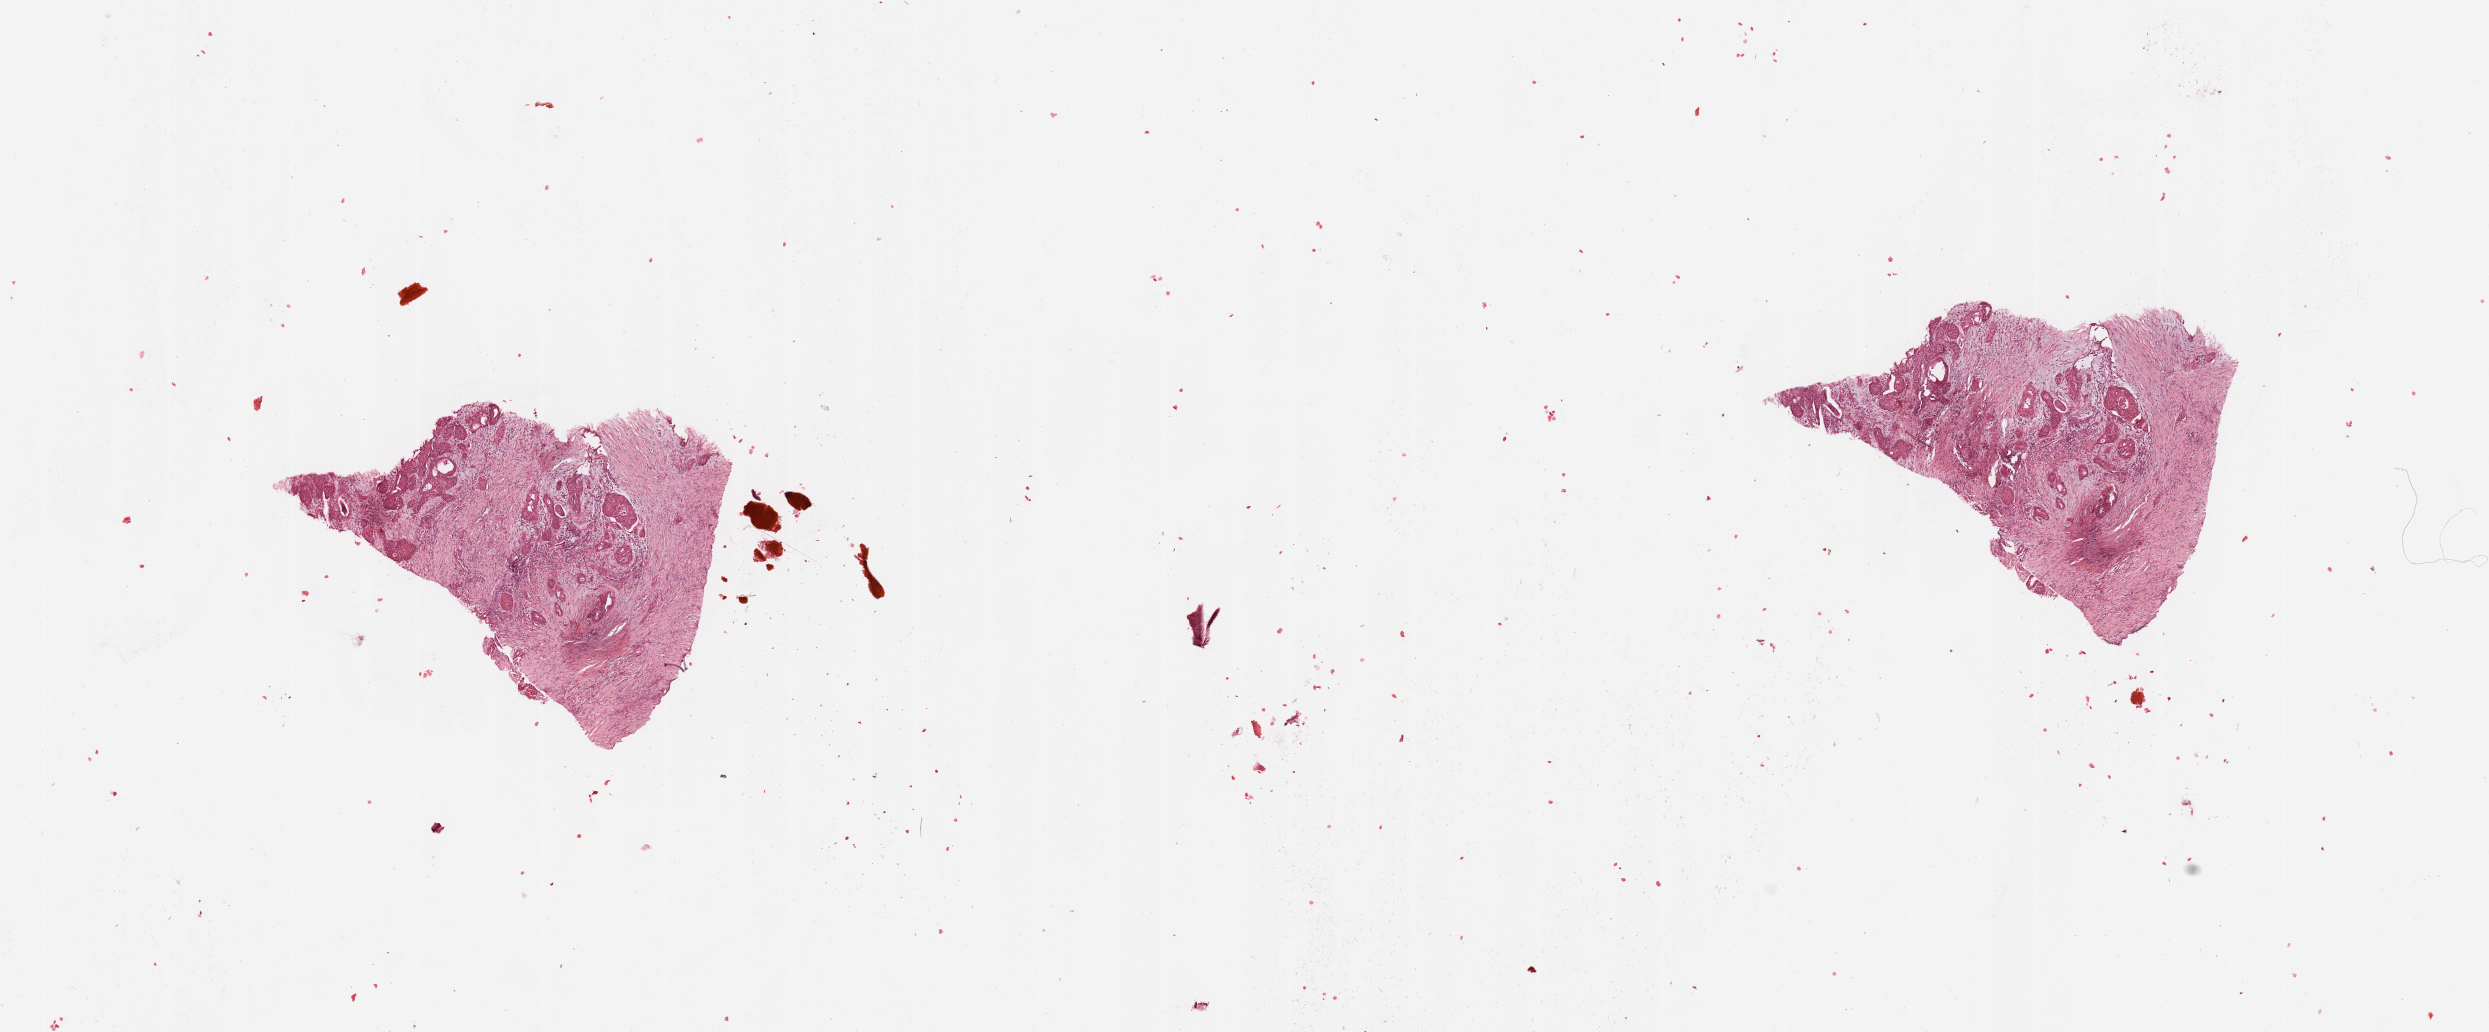
Digitized H&E tissue section (whole slide) — shown as a low-resolution overview of the whole scanned area (about 19.7 x 8.2 mm), tumour tissue sample, sampled site: pancreas. 60-year-old male patient. Pathologist review of this section (percent, as recorded): tumour nuclei 40%, necrosis 0%.
Histologic diagnosis: Infiltrating duct carcinoma, NOS.